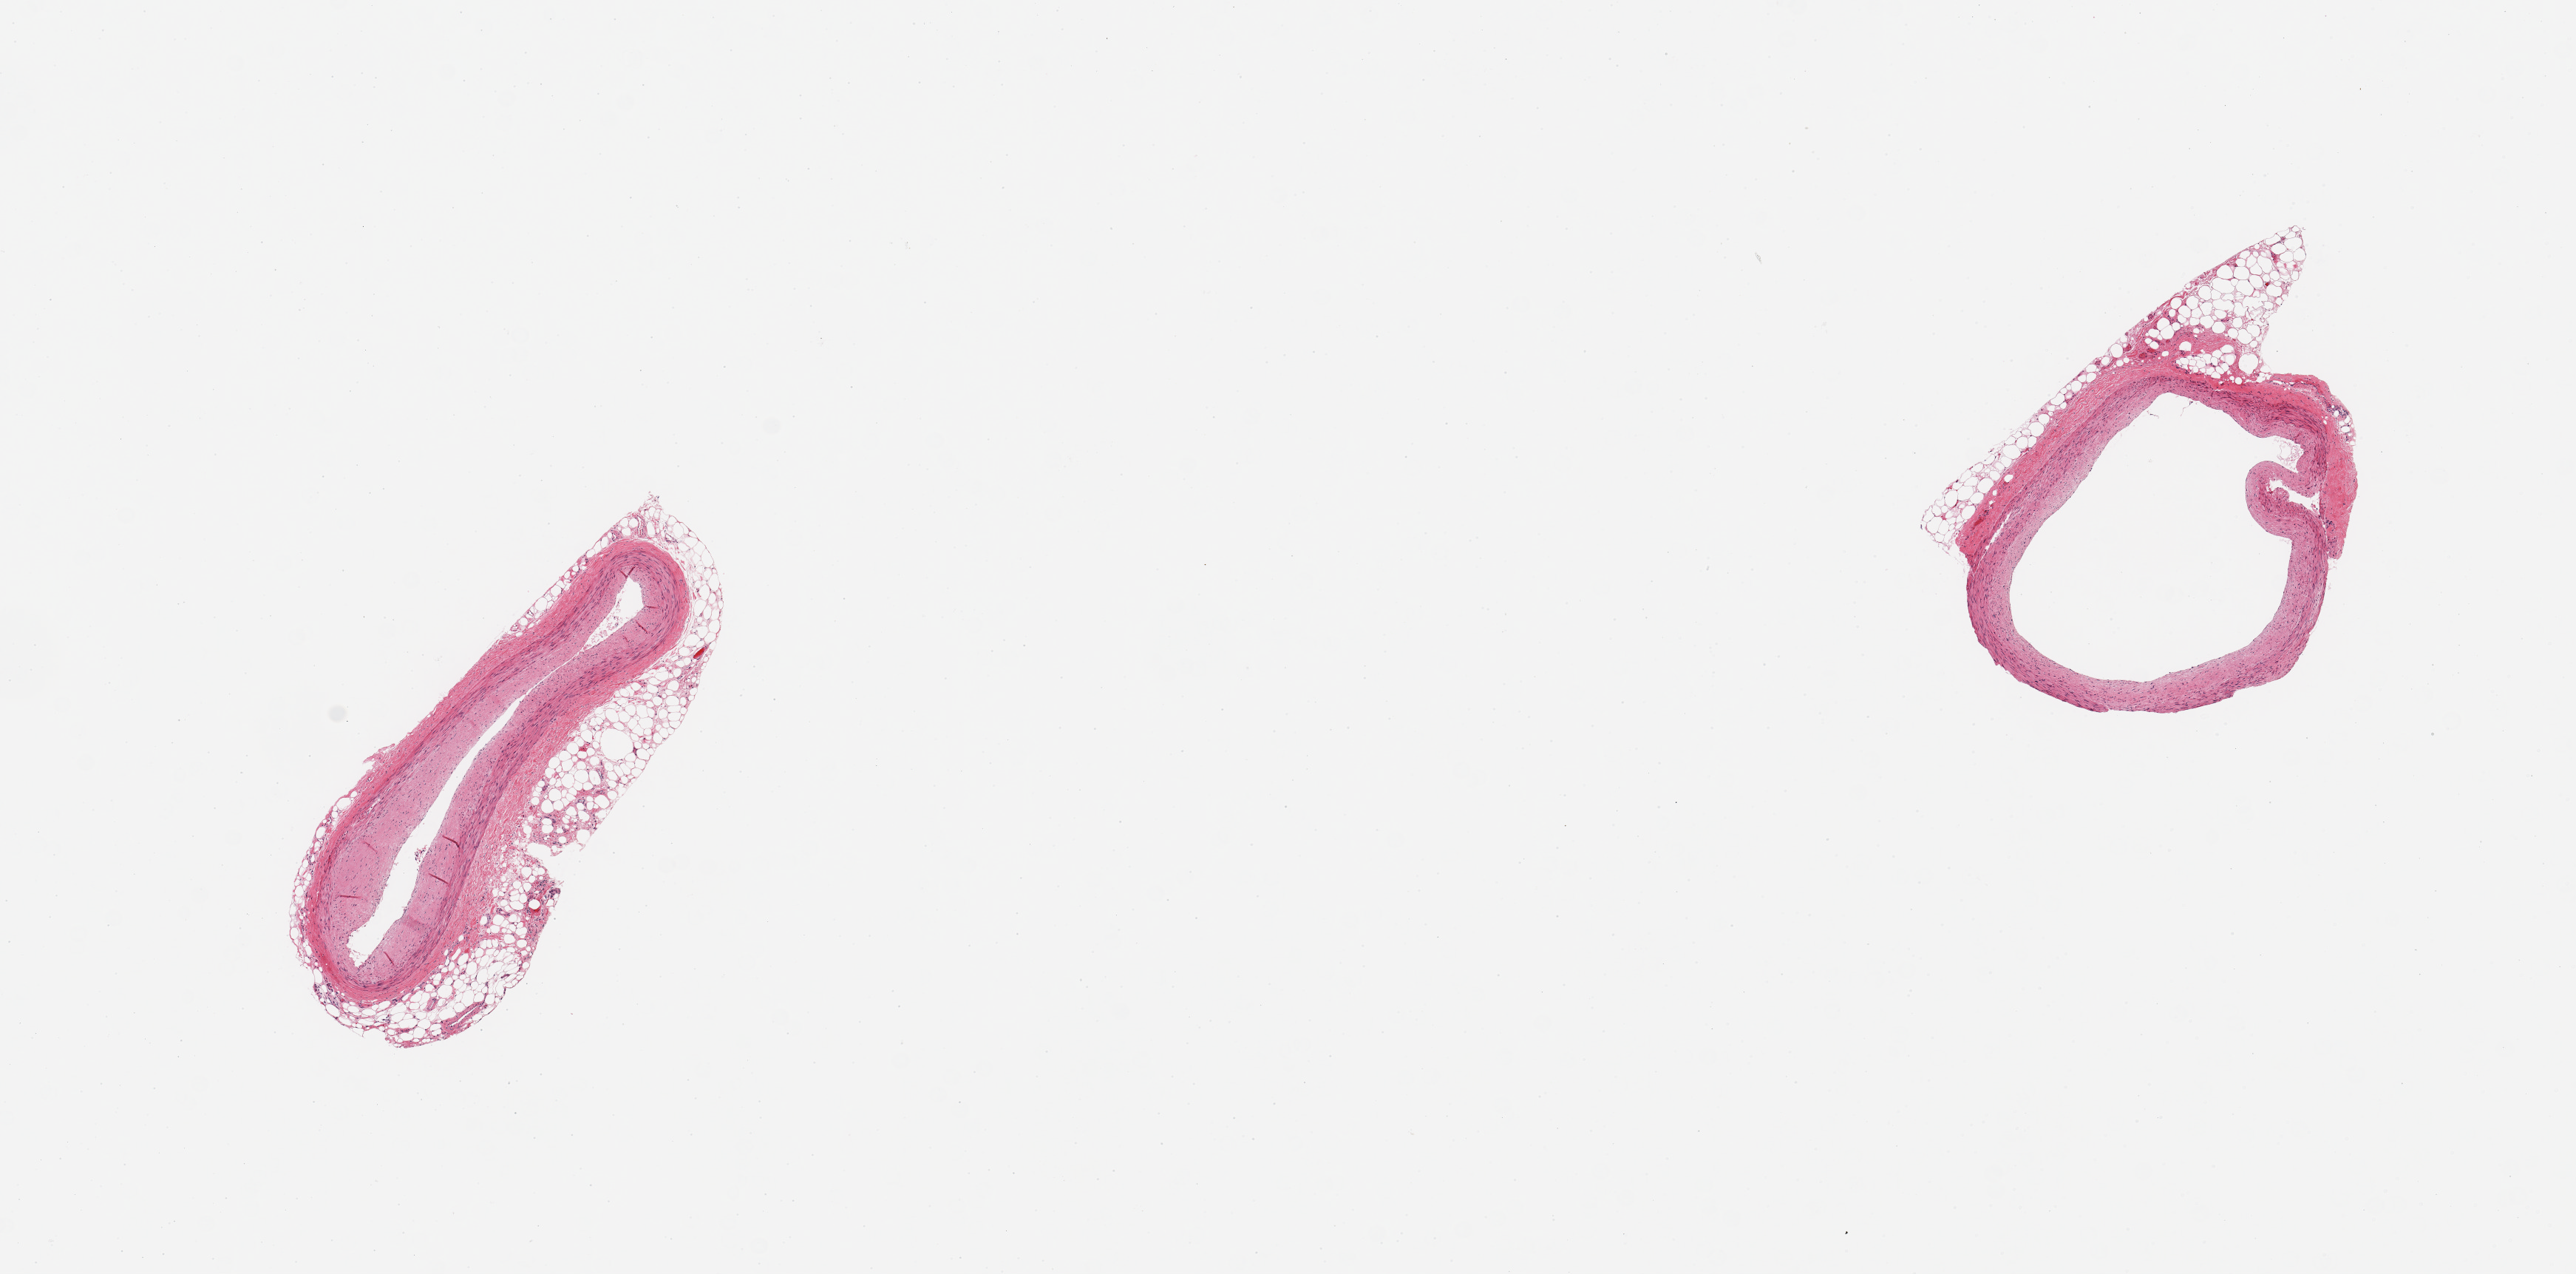
Hematoxylin and eosin (H&E) whole-slide image — low-resolution overview of the scanned area, about 13.8 x 6.8 mm. PAXgene-fixed, paraffin-embedded tissue. Target tissue: coronary artery. Tissue donor sample.
* review note (as recorded): 2 pieces; moderate plaque; 20% external fat